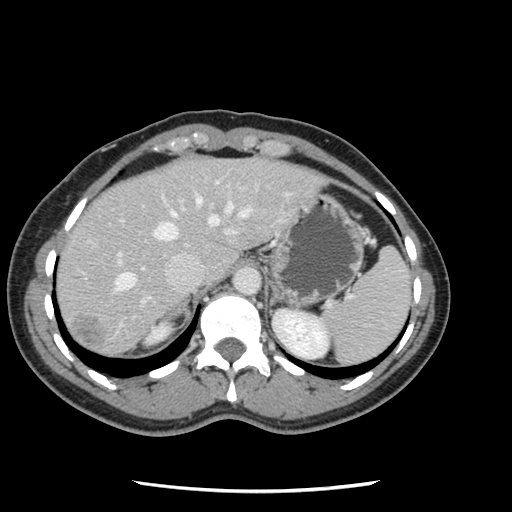
Contrast-enhanced abdominal CT, one axial slice; position 94 of 134 along the scan axis; 120 kVp; intravenous contrast given; soft-tissue window (W 400 / L 40 HU); 2.5 mm slice thickness; 512 × 512 image matrix, field of view 330 × 330 mm. Female patient, age 43 years. Case-level facts recorded for this patient, not image findings: diagnosis: colorectal cancer liver metastases, imaged before liver resection; multiple liver metastases: yes; largest metastasis: 3.4 cm; disease in both lobes: yes.
Outlined on this slice (outlined manually by an expert reader):
- hepatic veins: box from (x=115, y=194) to (x=251, y=292) px
- liver: (x=57, y=158)–(x=320, y=357)
- planned liver remnant (the part of the liver to remain after resection): (x=57, y=164)–(x=193, y=309)
- portal vein (with intrahepatic branches): (x=83, y=180)–(x=238, y=308)
- liver metastasis: (x=71, y=317)–(x=104, y=351)